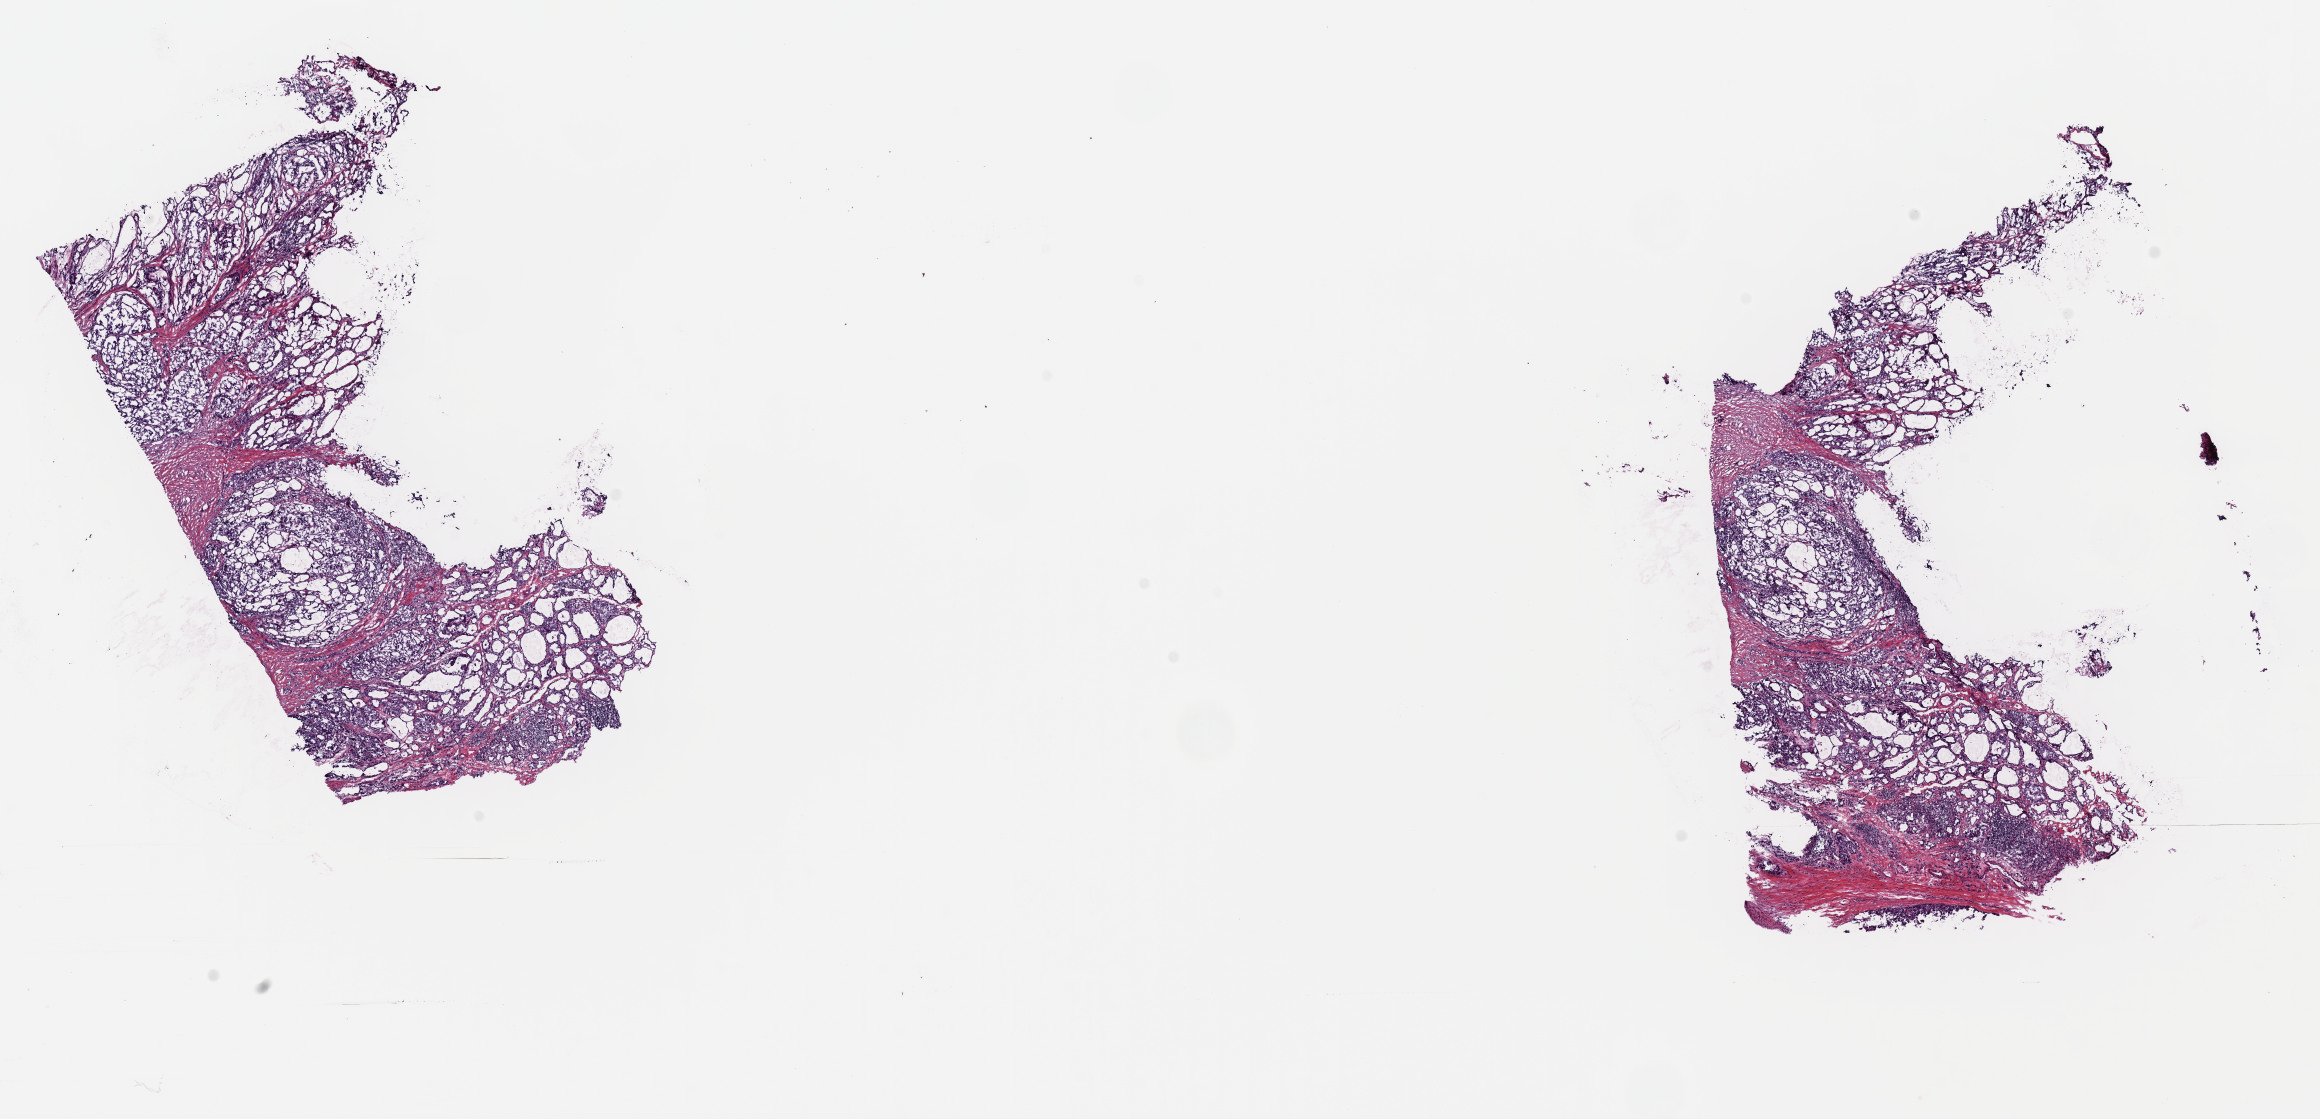
H&E-stained whole-slide image, a low-resolution overview of the entire scanned area, about 18.3 x 8.8 mm; frozen section from the top of the tissue portion; sample: primary tumour, thyroid. Female patient; age at initial diagnosis 28 years. Slide review estimates, as recorded: tumour cells 100%, tumour nuclei 65%, normal cells 0%, stromal cells 0%, necrosis 0%. Inflammatory infiltration, as recorded: lymphocyte infiltration 0%, monocyte infiltration 0%, neutrophil infiltration 0%.
AJCC pathologic stage: I (6th edition). Histologic diagnosis: Papillary adenocarcinoma, NOS (thyroid gland).